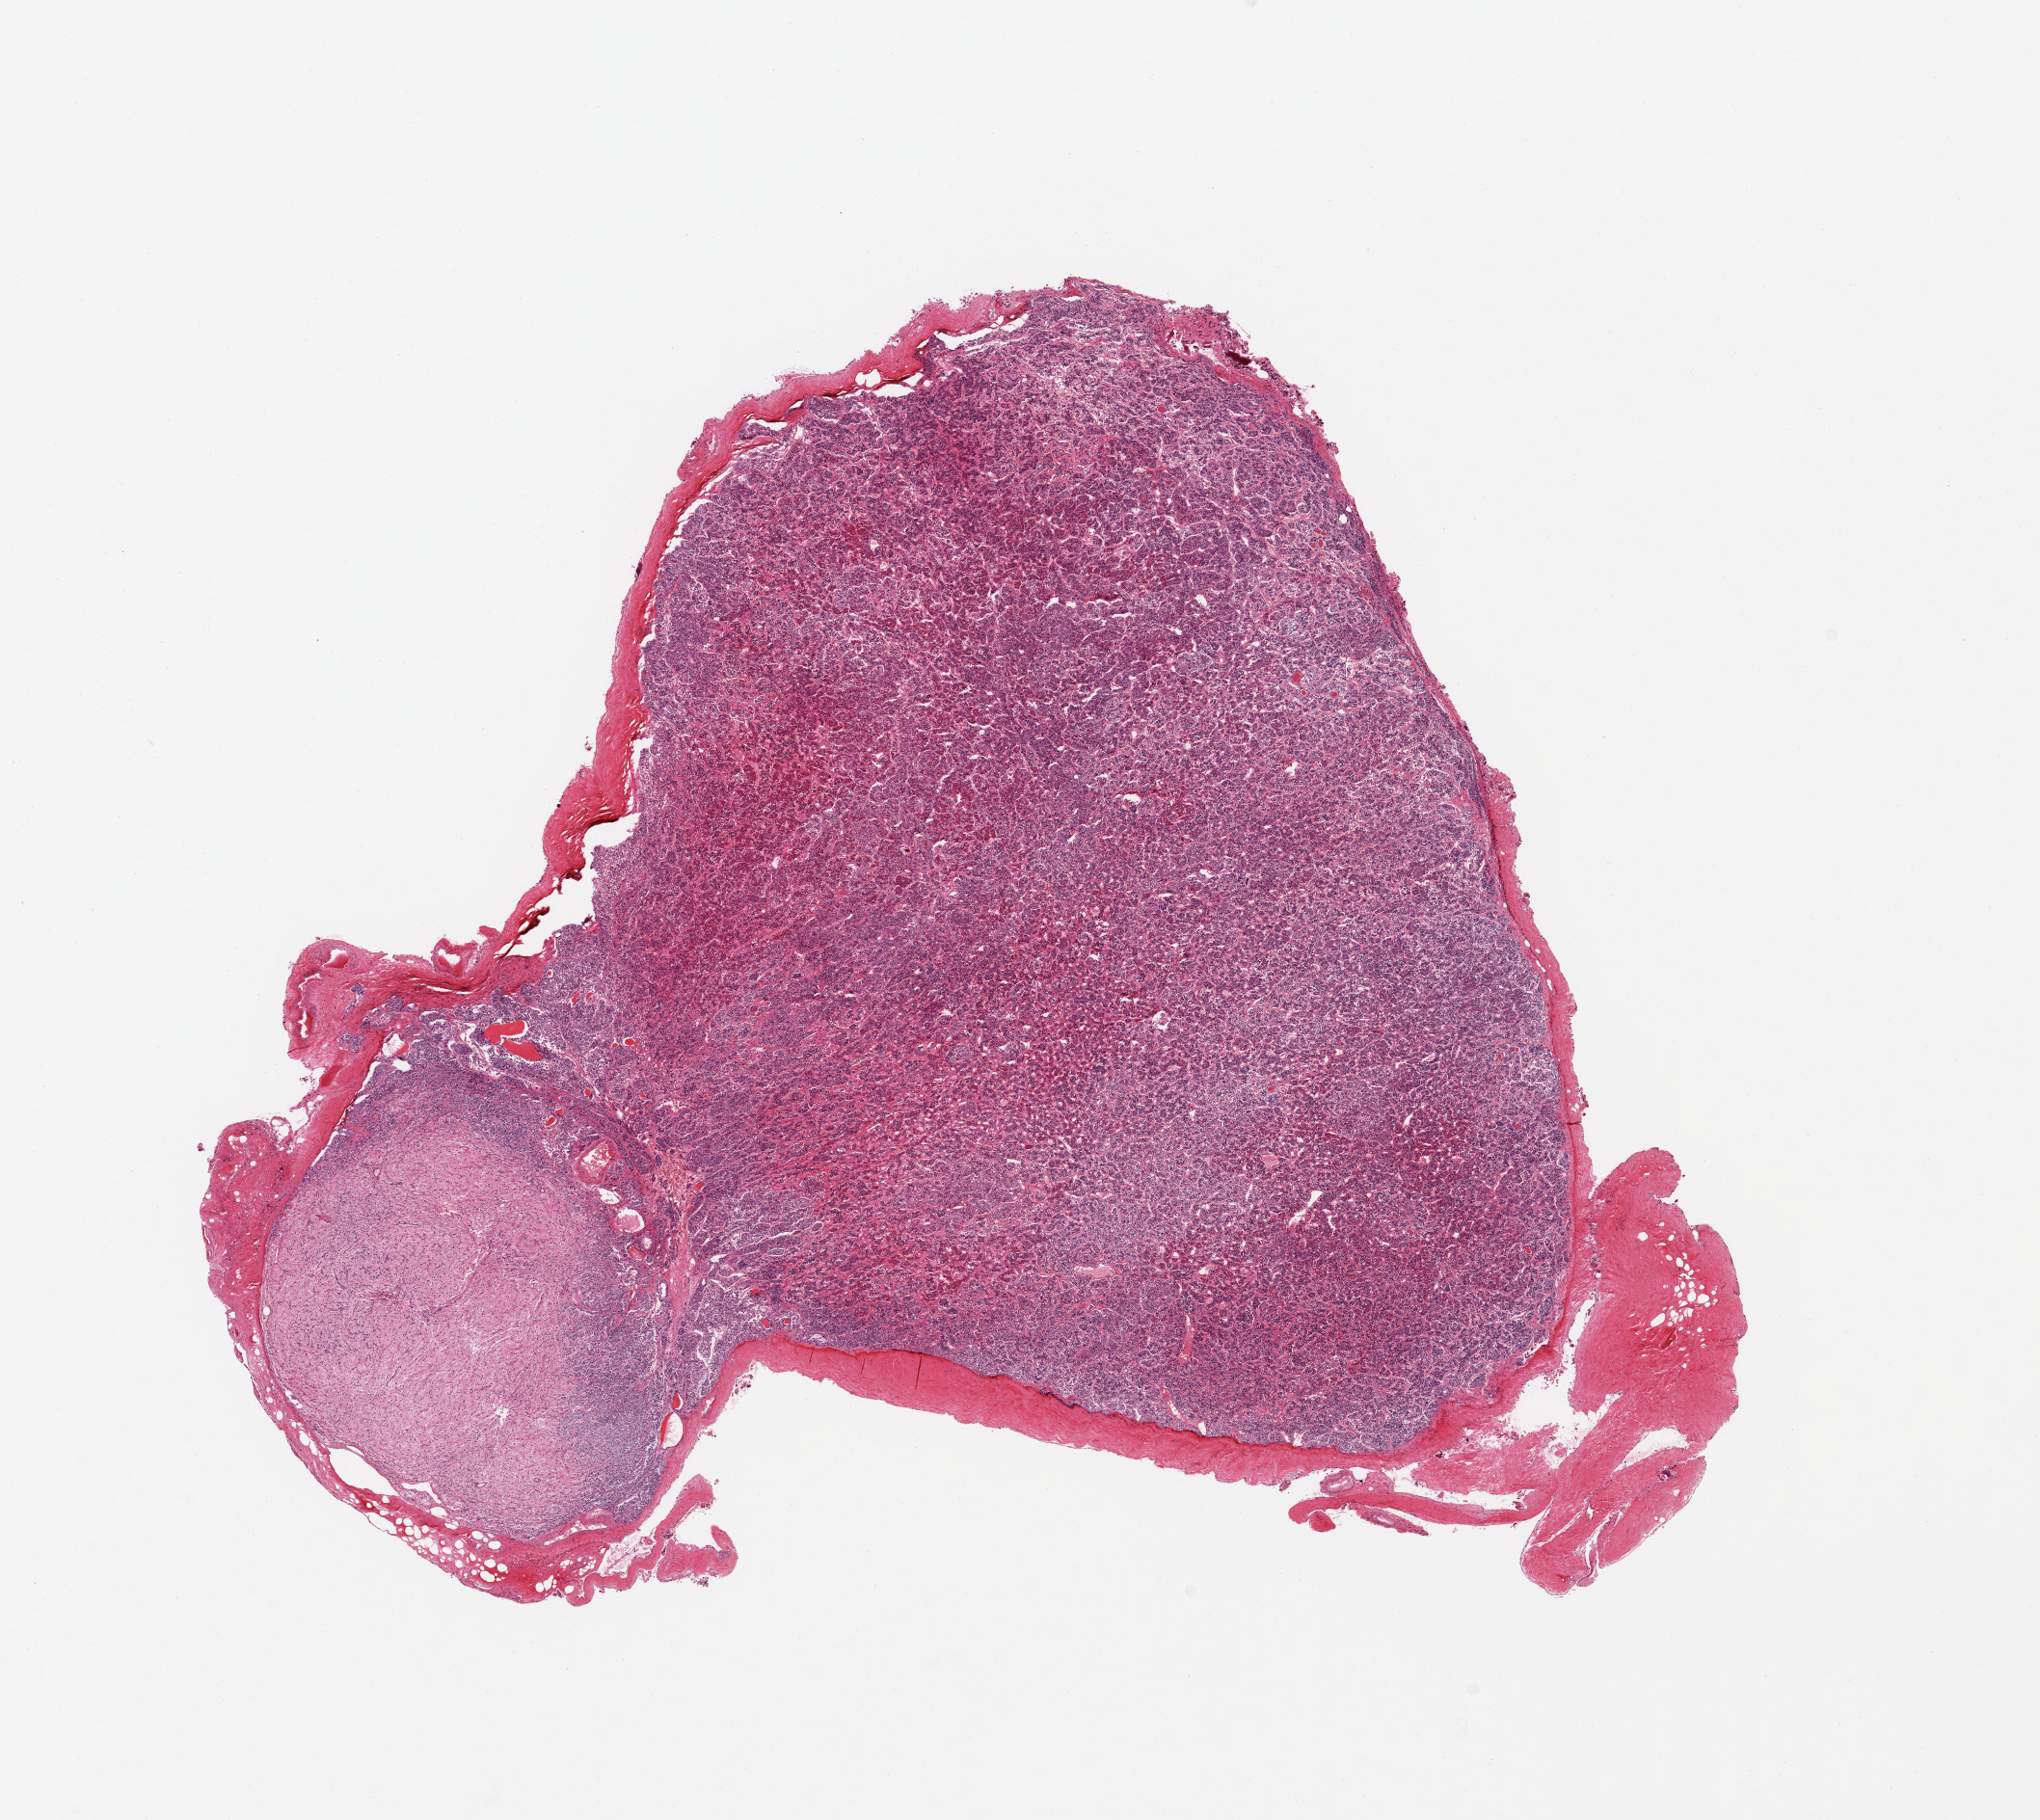
Haematoxylin and eosin whole-slide image, brightfield — whole scanned area (about 16.7 x 14.9 mm) shown as a low-resolution overview, PAXgene-fixed paraffin-embedded (PFPE) section, sampled site (target tissue): pituitary, tissue donor sample. Donor sex: male.
Review note (as recorded): 1 piece; anterior and posterior lobes represented.